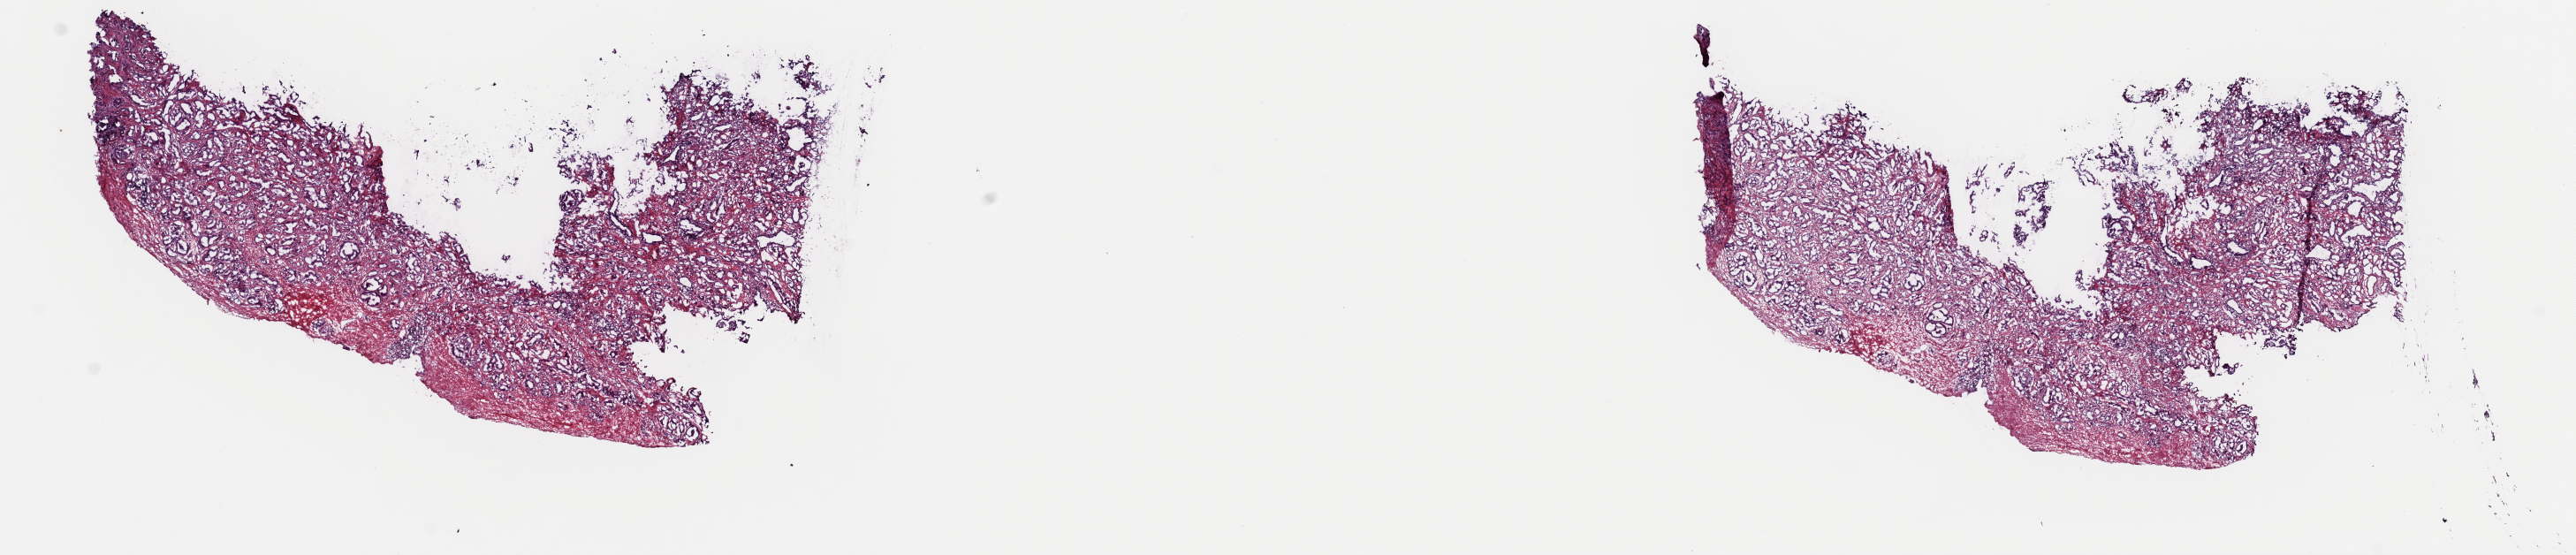
Whole-slide histology image, H&E-stained, low-resolution overview of the scanned area, about 23.0 x 5.0 mm, frozen section from the top of the tissue portion, primary tumour sample from the prostate. Patient: male, age at initial diagnosis 54 years. Gleason score: 7 (3+4). Slide review estimates, as recorded: tumour cells 100%, tumour nuclei 65%, normal cells 0%, stromal cells 0%, necrosis 0%. Infiltration values recorded for this section: lymphocyte infiltration 1%, monocyte infiltration 0%, neutrophil infiltration 0%.
Laterality: left. Diagnosis: Adenocarcinoma, NOS (prostate gland).